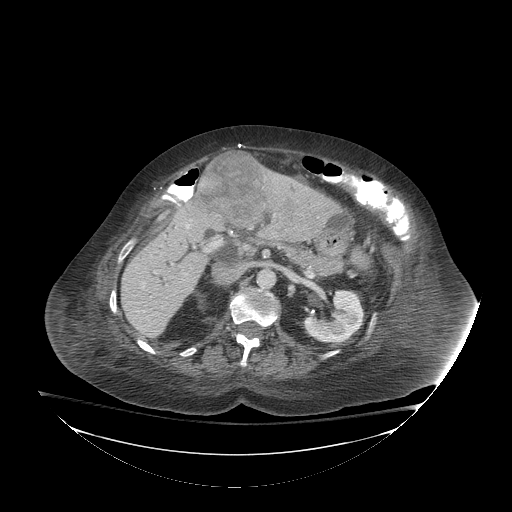
Contrast-enhanced abdominal CT (liver protocol), one axial slice; position 42 of 81 along the scan axis; 140 kVp; soft-tissue window (W 400 / L 40 HU); 512 × 512 image matrix. Case-level facts recorded for this patient, not image findings: diagnosis: hepatocellular carcinoma (patient treated with transarterial chemoembolisation; whether this scan precedes or follows treatment is not stated here); TNM stage (as recorded): Stage-I; Child-Pugh class: B; tumour nodularity: uninodular.
Outlined on this slice (semi-automatically segmented with operator editing):
- liver parenchyma outside the tumour (the mass and vessels are separate outlines, so this box may not span the whole liver): bounding box <120,168,338,338> (left, top, right, bottom; pixels)
- mass: <197,152,270,227>
- liver vessels: <186,224,219,246>